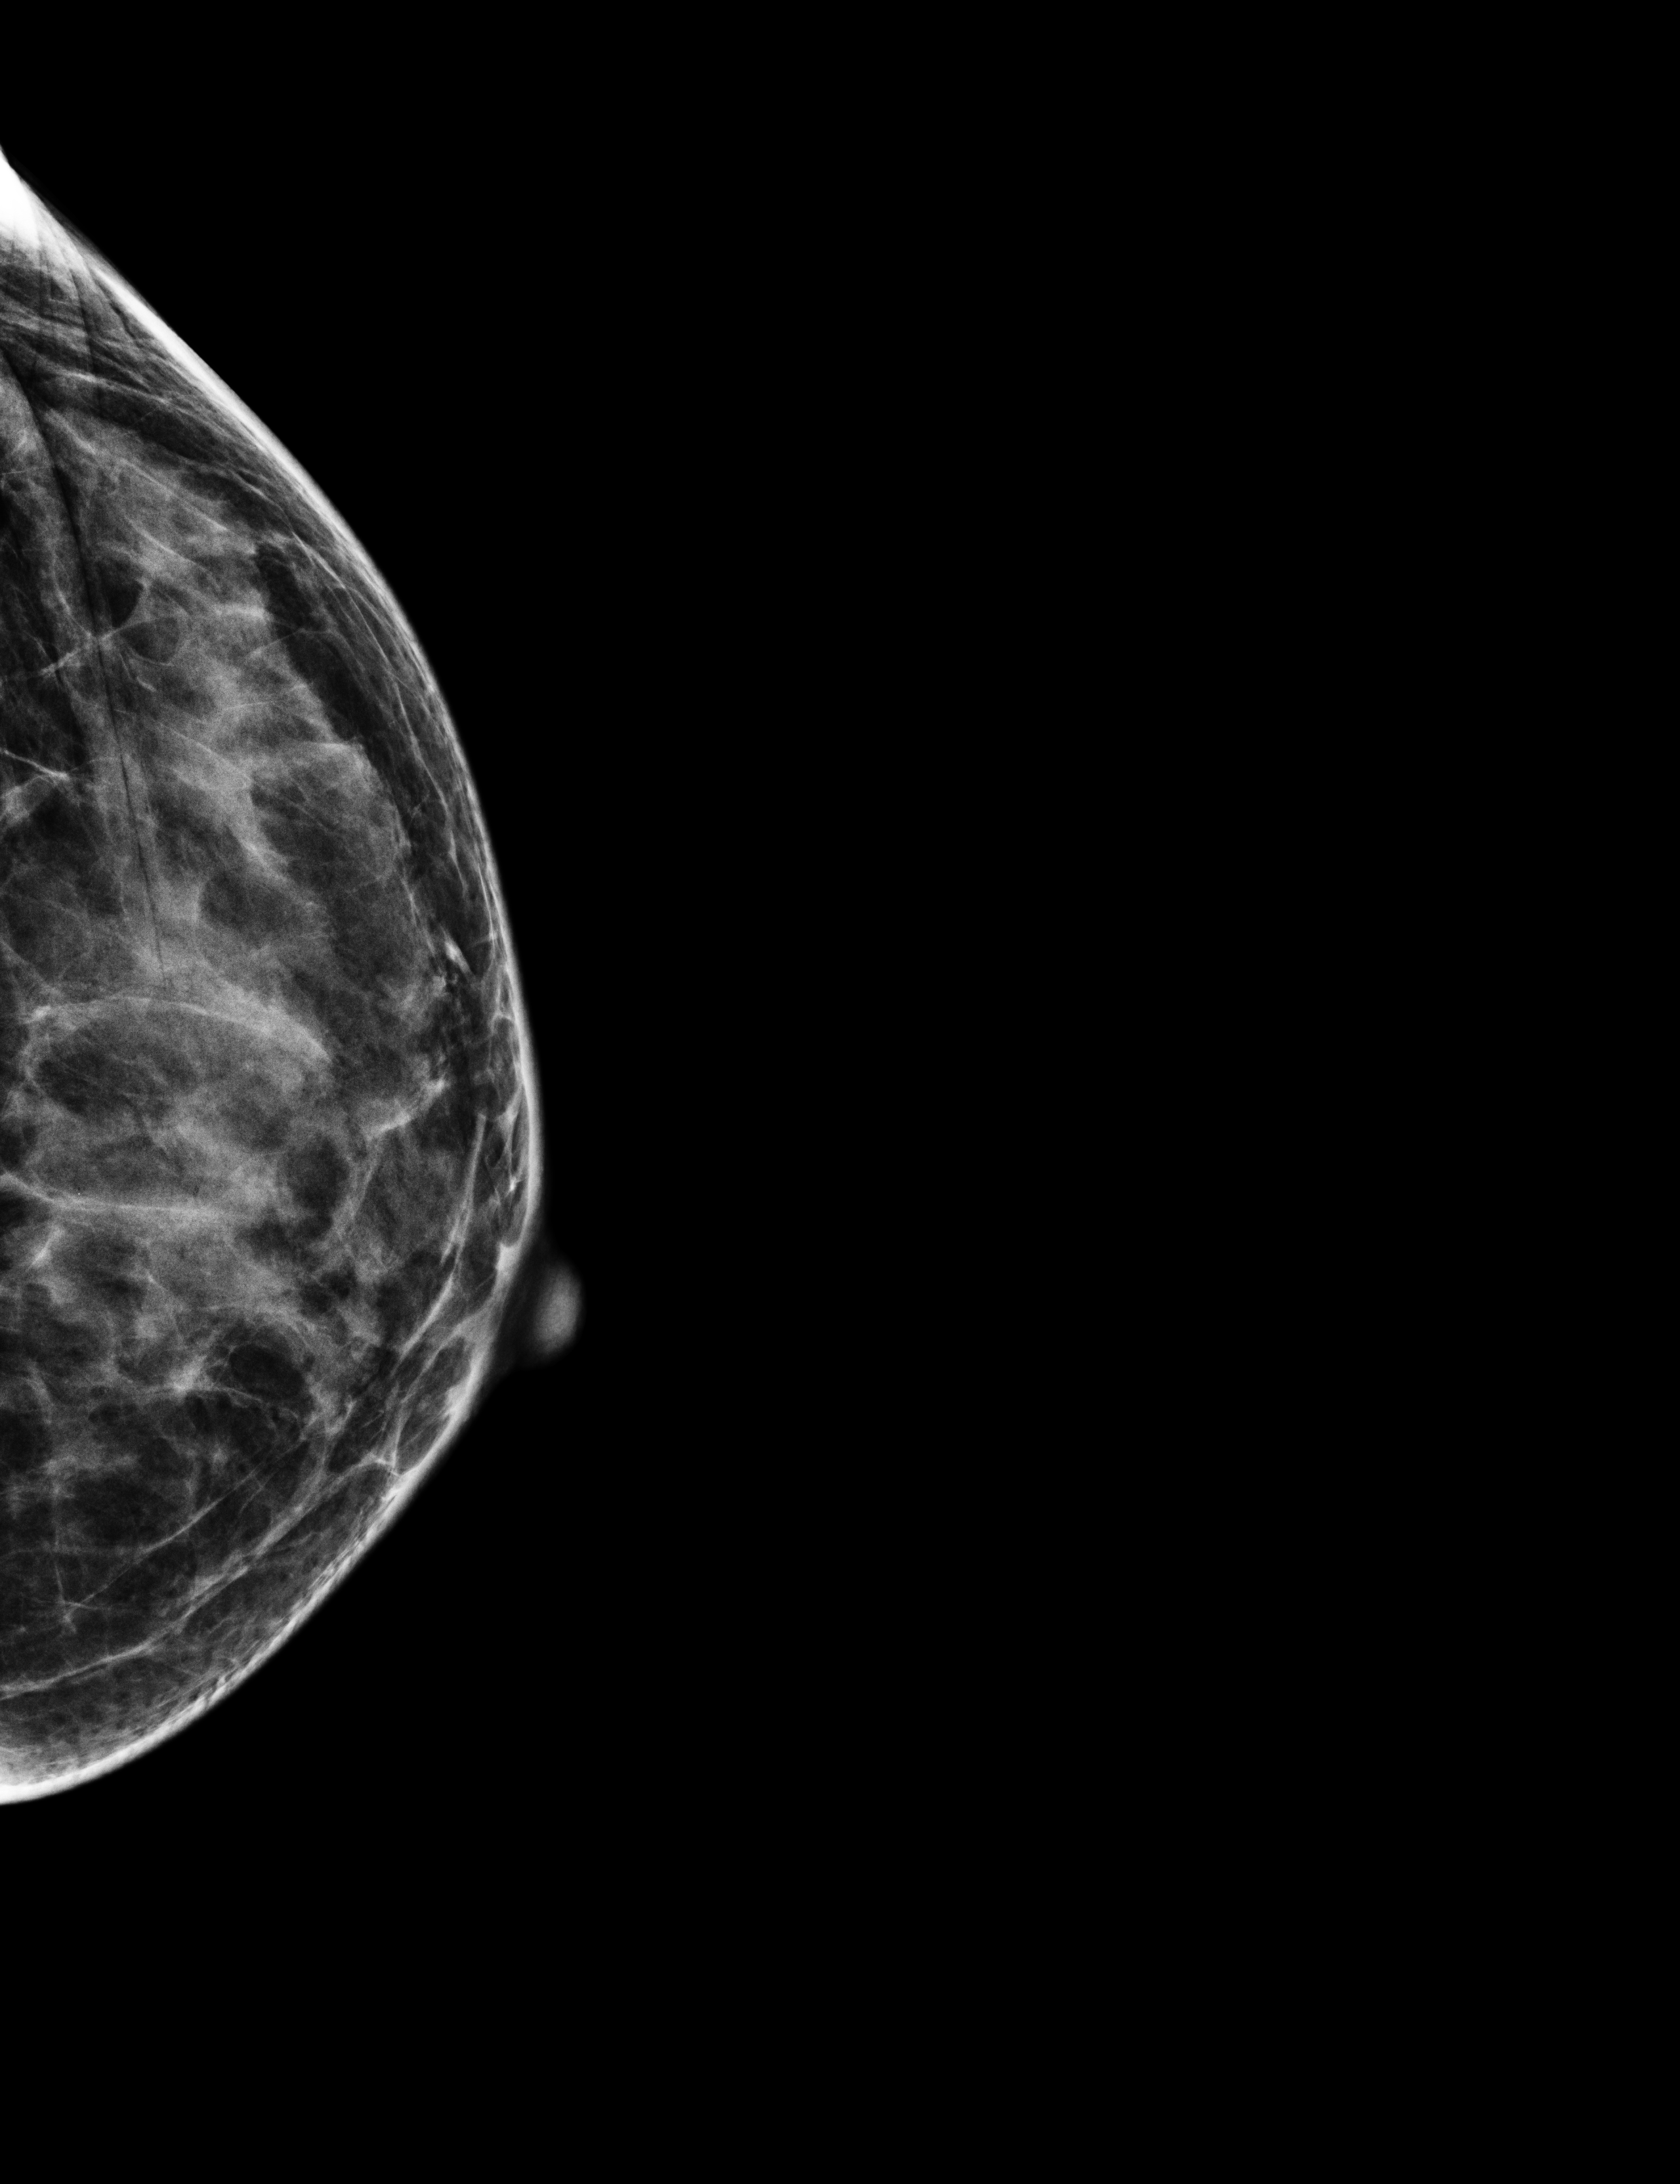
Full-field digital mammogram (FFDM), left breast, laterally exaggerated craniocaudal (XCCL) view, annual screening mammography examination, compressed breast thickness 32 mm. Patient: female, 52 years.
BI-RADS breast density category at the screening exam (both breasts, scale 1–4): 3. Final BI-RADS category for the screening round (tomosynthesis exam, both breasts): category 1. Recall: no recall after this screen.